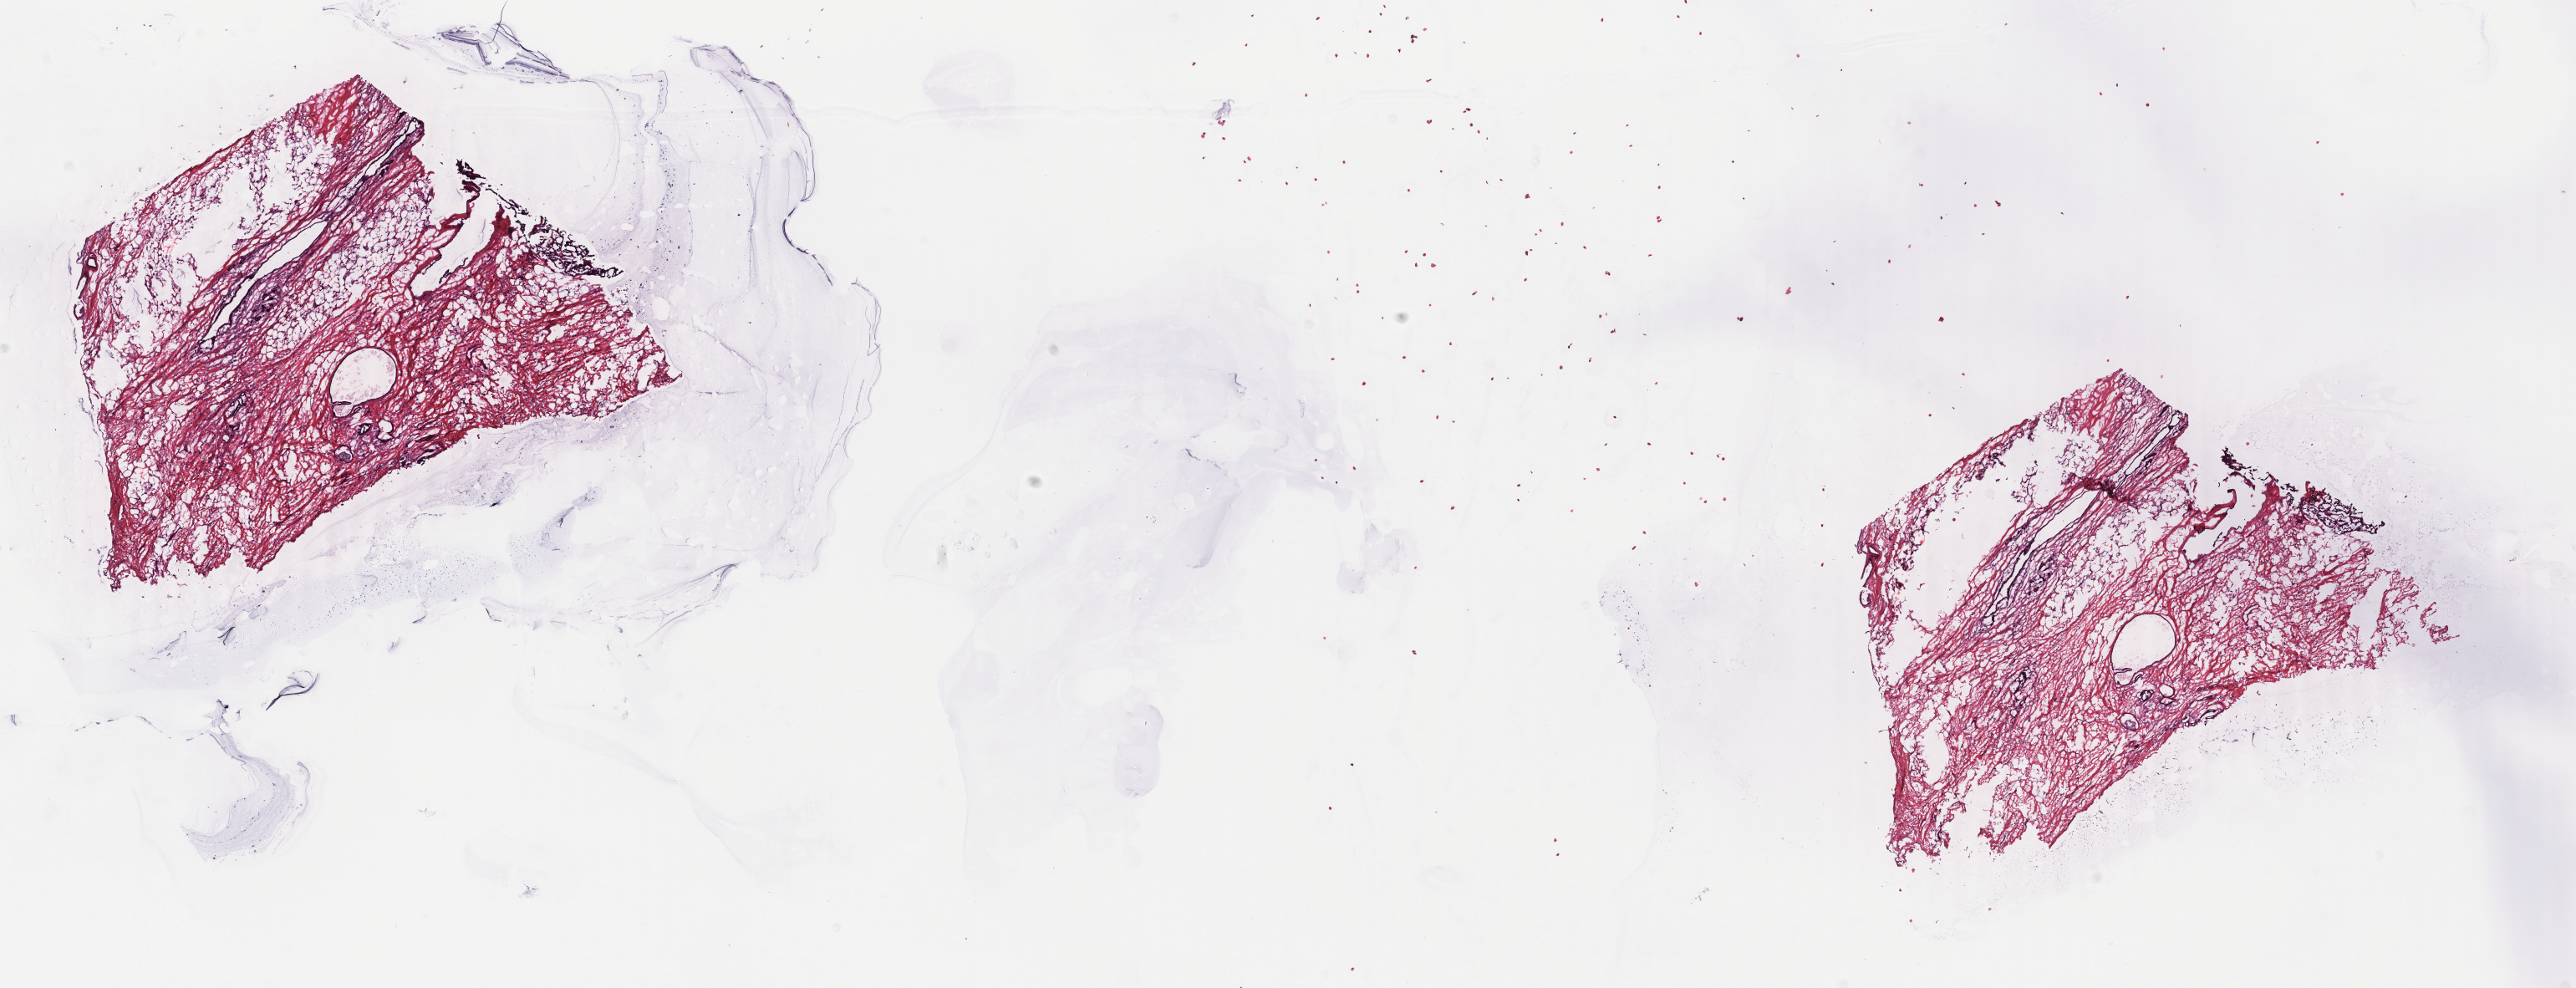
H&E whole-slide image, shown as a low-resolution overview of the whole scanned area (about 24.5 x 9.4 mm, from a 40x scan); frozen section from the bottom of the tissue portion; breast, primary tumour sample. Female patient; age at initial diagnosis 68 years. Composition of this section per pathologist review: tumour cells 30%, tumour nuclei 40%, normal cells 6%, stromal cells 64%, necrosis 0%. Inflammatory infiltration, as recorded: lymphocyte infiltration 1%, monocyte infiltration 0%, neutrophil infiltration 0%.
Diagnosis: Lobular carcinoma, NOS. Laterality: right. AJCC pathologic stage: IIB (4th edition). Lymph nodes positive (case pathology): 0 of 14 examined.